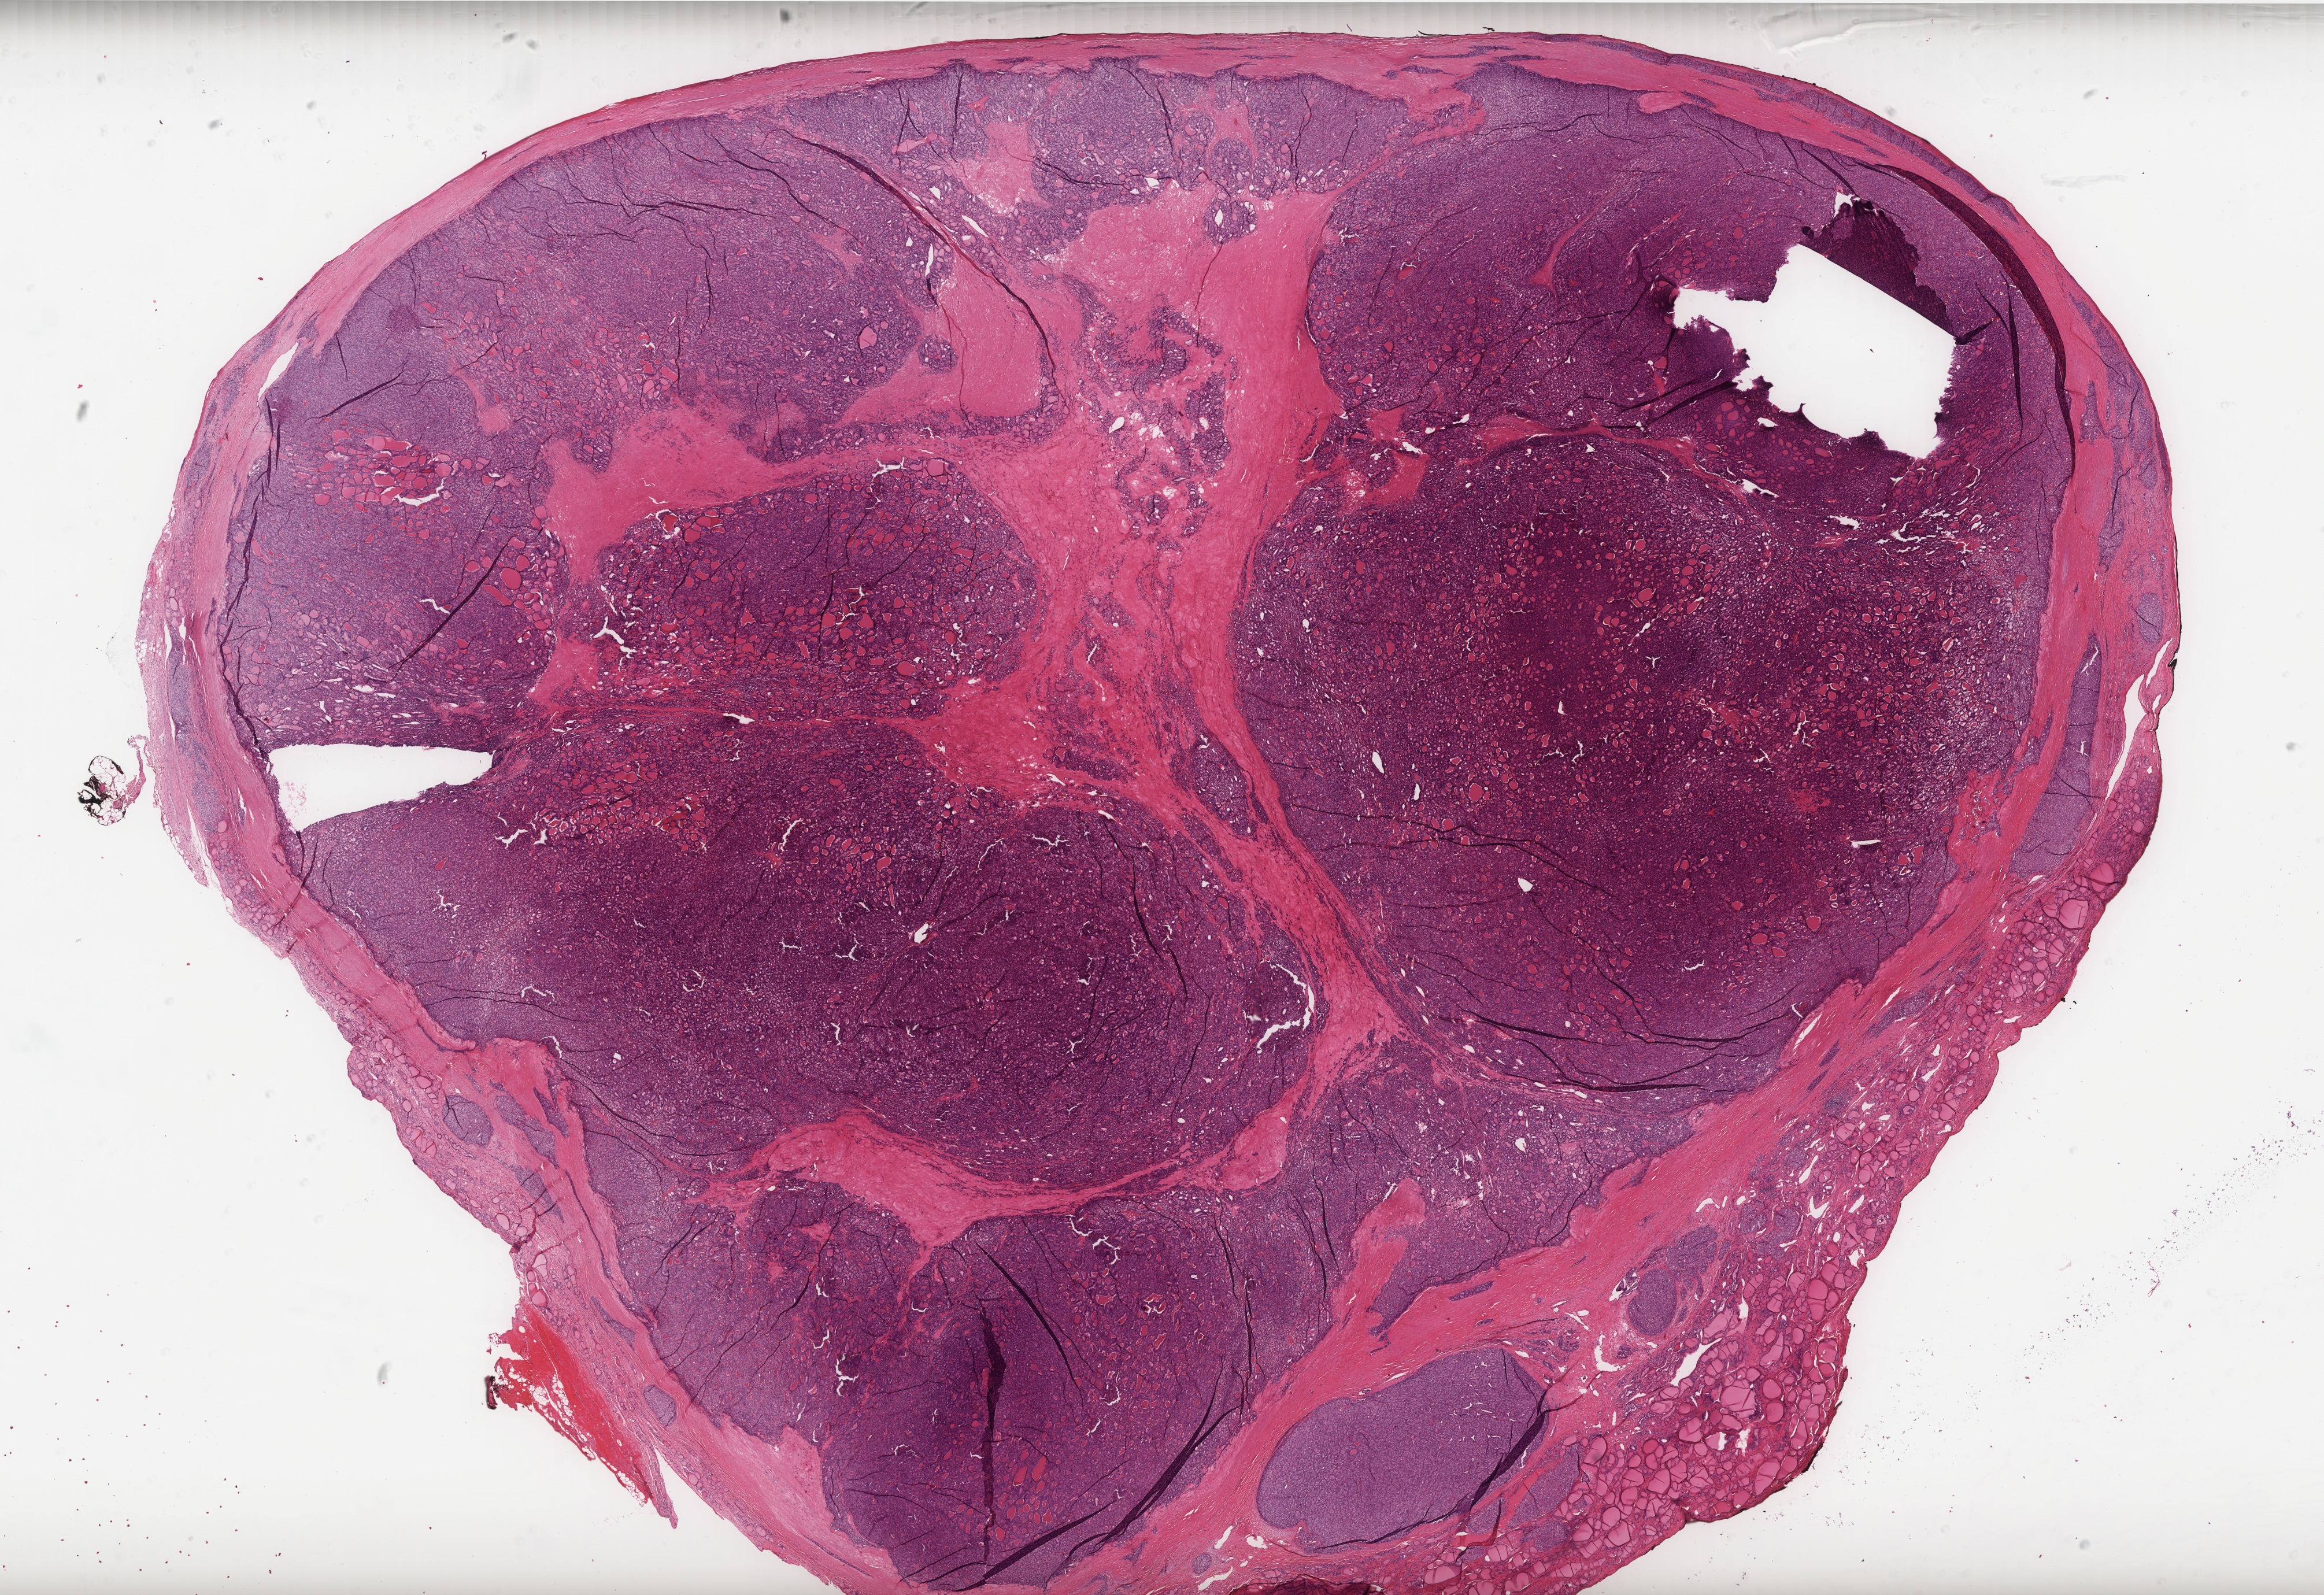
Whole-slide histology image, H&E-stained, whole scanned area (about 32.2 x 22.1 mm) shown as a low-resolution overview. FFPE section. Primary tumour sample from the thyroid. Male patient; age at initial diagnosis 57 years.
• laterality: left
• AJCC pathologic stage: IVC
• pathologic diagnosis: Follicular adenocarcinoma, NOS